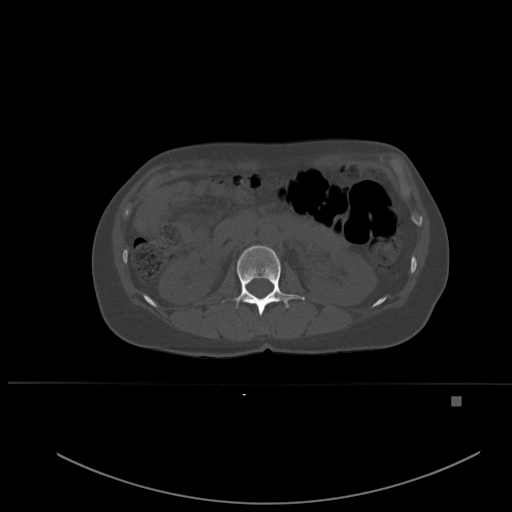
CT including the spine, one axial slice; position 233 of 651 along the scan axis; bone window (W 1800 / L 400 HU); 1.5 mm slice thickness; 512 × 512 image matrix. Female patient, age 49 years. Case-level facts recorded for this patient, not image findings: primary cancer: breast; vertebrae with lytic lesions (as recorded): L3, T12, L4.
Outlined on this slice (semi-automatically segmented with operator editing):
- L1 vertebra: bounding box (x1, y1, x2, y2) in pixels: (222, 245, 305, 316)